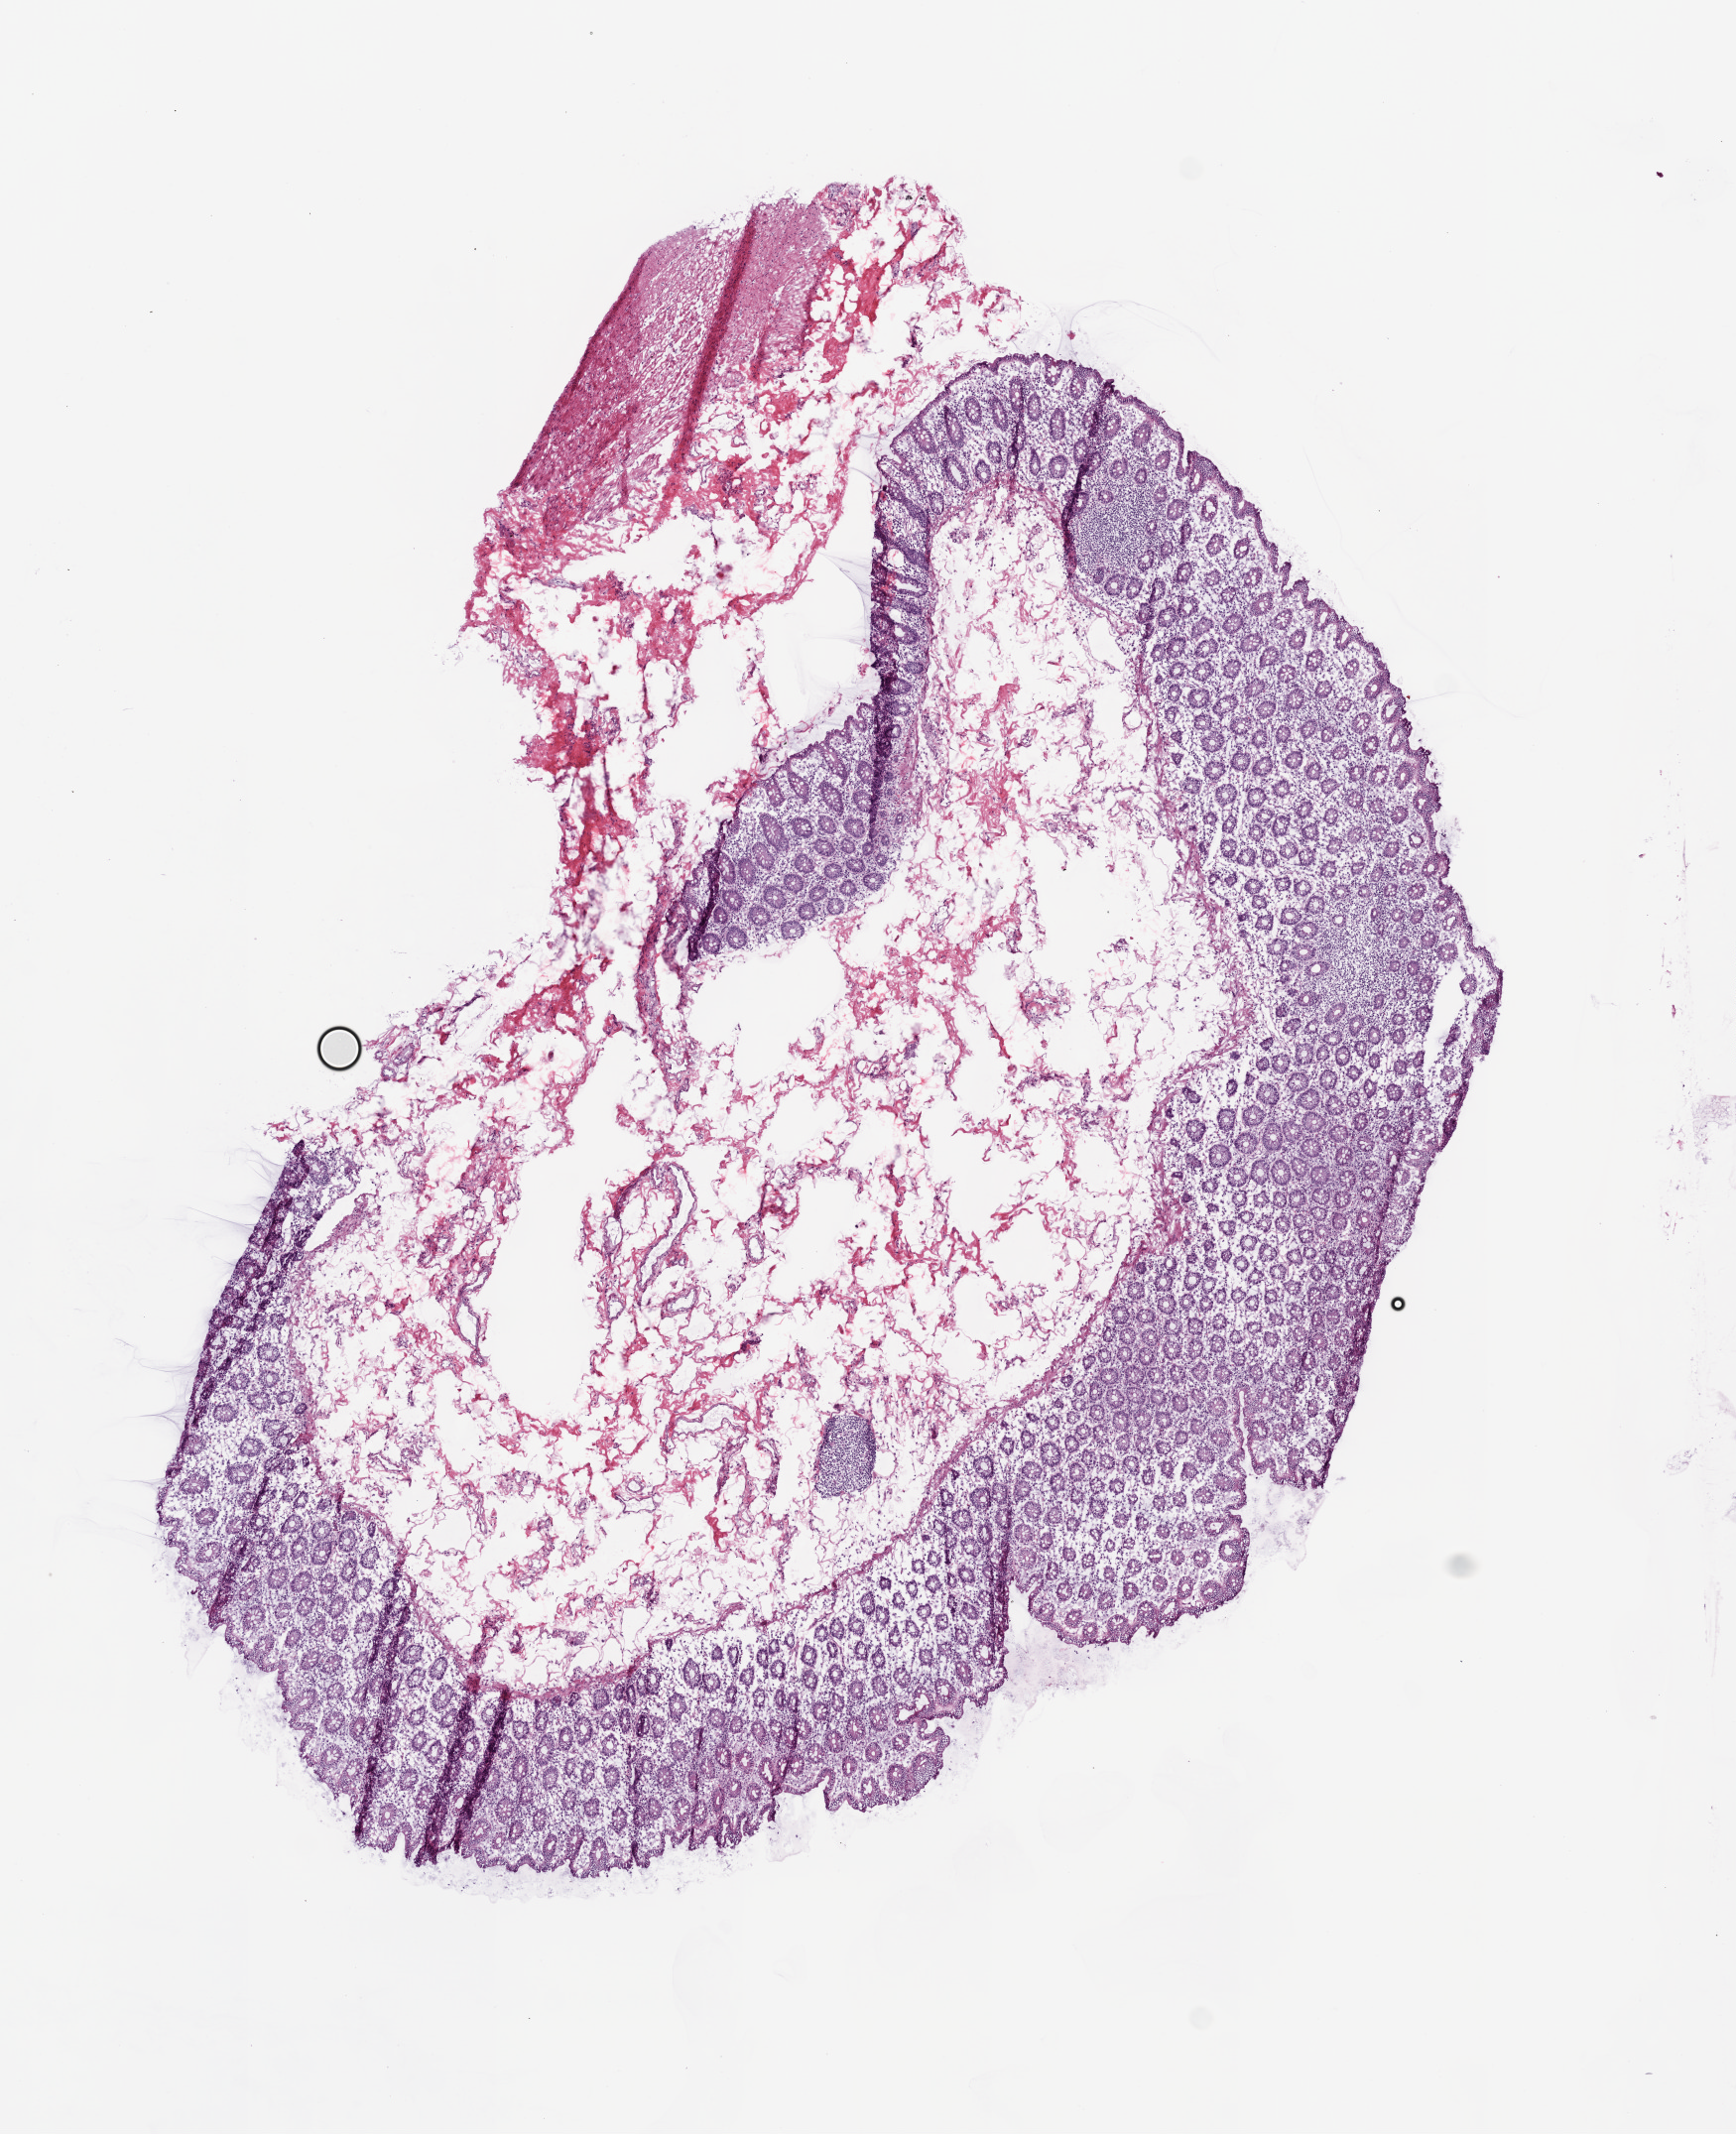
H&E-stained whole-slide image, a low-resolution overview of the entire scanned area, about 7.0 x 8.6 mm (acquisition: 20x scan); frozen section from the top of the tissue portion; colon, solid tissue normal (non-tumour tissue) sample. Male patient; age at initial diagnosis 73 years.
This section: solid tissue normal (non-tumour) sample from the same patient. Patient diagnosis: Adenocarcinoma, NOS.